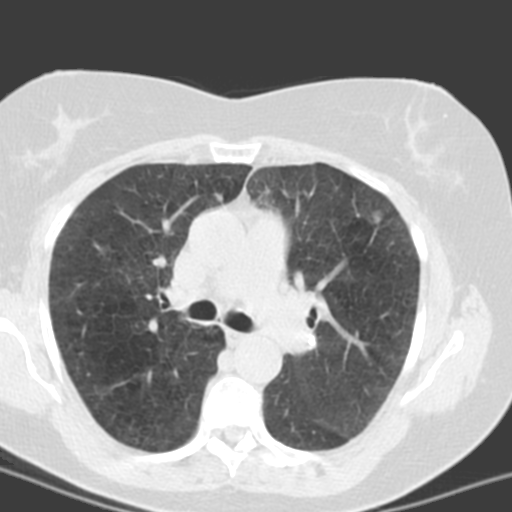
Low-dose screening chest CT, one axial slice. 120 kVp. Lung window (W 1500 / L -600 HU). 512 × 512 image matrix, field of view 290 × 290 mm.
Structures marked on this image (outlined manually by an expert reader):
- lesion 1 (tumor, lower lobe of left lung): box from (x=372, y=210) to (x=383, y=223) px